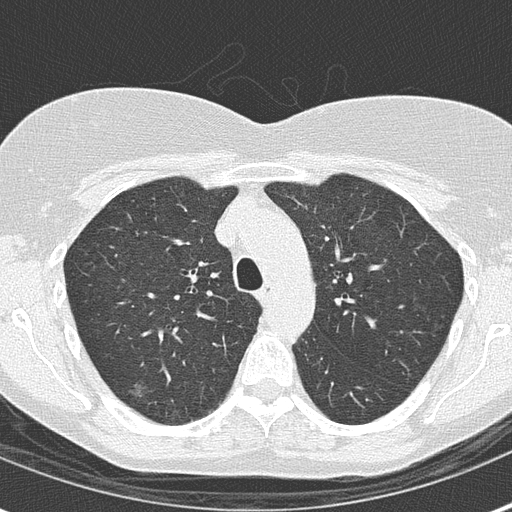
Axial slice from a low-dose chest CT screening exam, first (baseline) screen, lung window (W 1500 / L -600 HU), 2 mm slice thickness, lung (sharp) reconstruction kernel (B50f), slice 45 of 147 in the series, 512 × 512 image matrix. Female participant, aged 56 years at enrolment. Current smoker at enrolment.
Expert reader's lesion annotation, bounding box [x1, y1, x2, y2] px = [111, 367, 160, 421]. The screening reader recorded 2 non-calcified nodules or masses ≥4 mm on this exam (right upper lobe, left upper lobe); which of them this box marks is not recorded. Official screen result: positive, change unspecified: nodule(s) >= 4 mm or enlarging nodule(s), mass(es), or other non-specific abnormalities suspicious for lung cancer. Later outcome: lung cancer diagnosed 457 days after this screen (after the second annual screen) — bronchiolo-alveolar adenocarcinoma, NOS, right upper lobe, well differentiated (G1), stage IA (AJCC 6th edition), 15 mm at pathology.